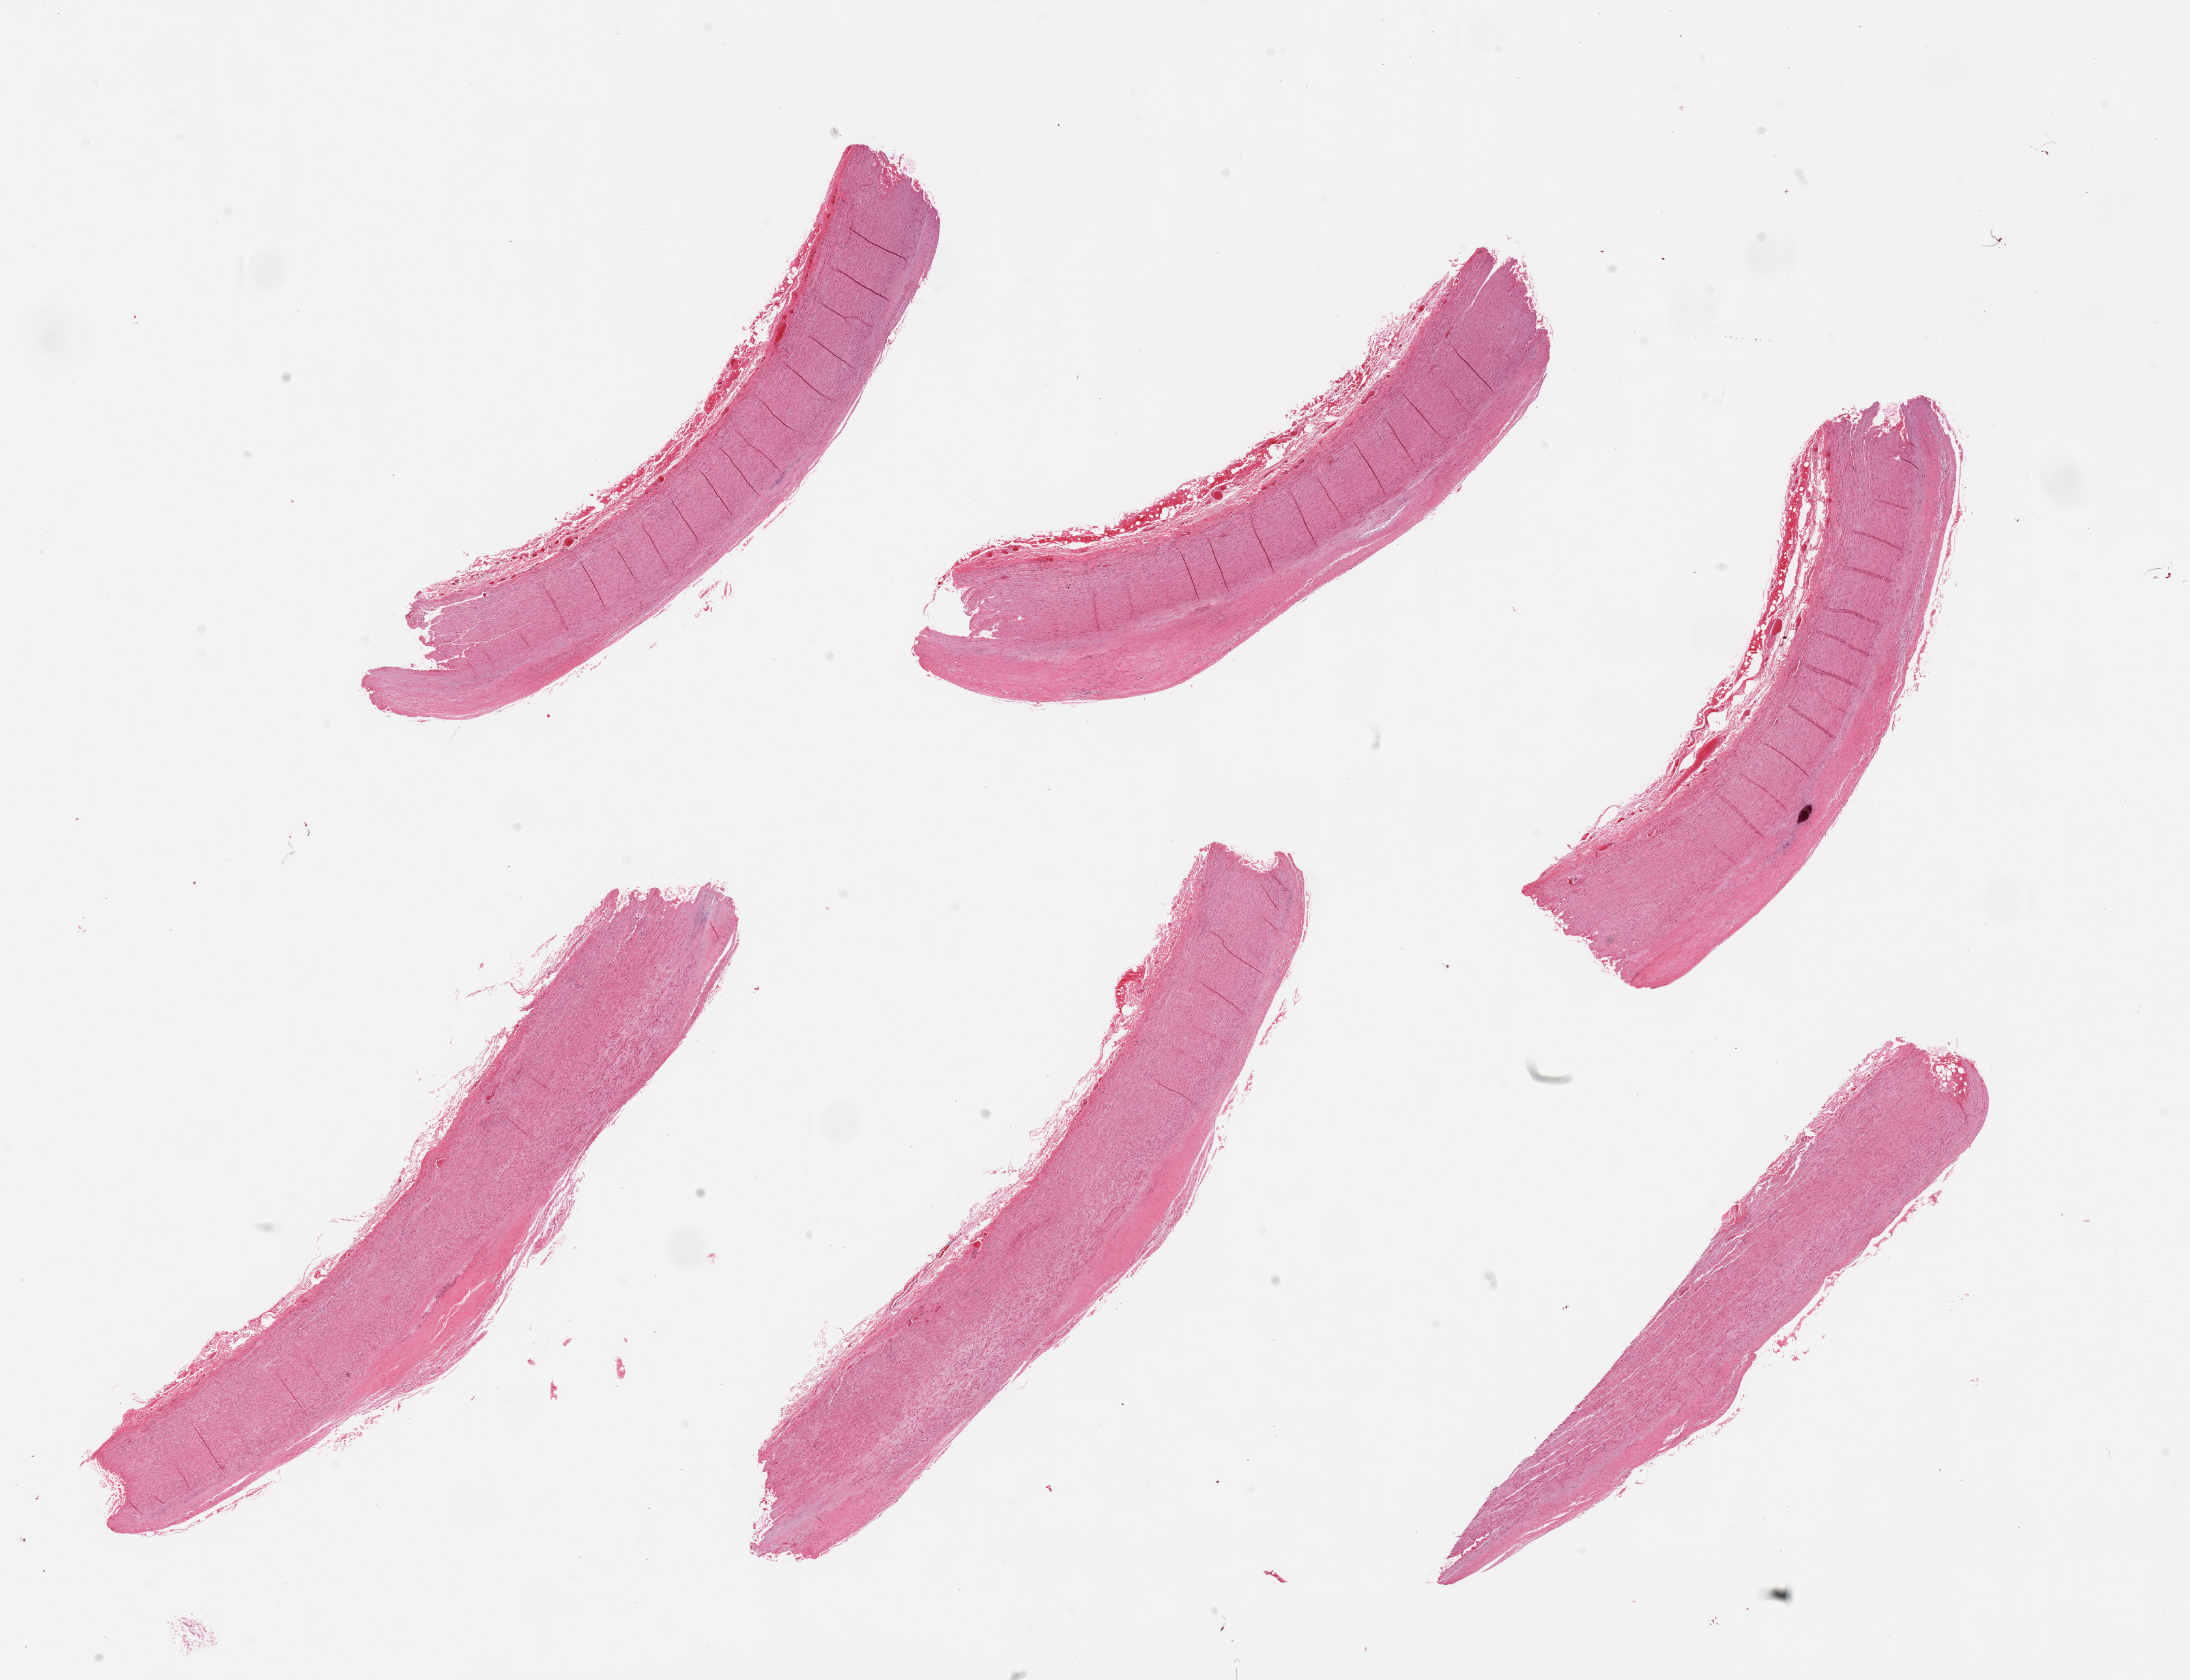
Whole-slide image, H&E stain, brightfield — whole scanned area (about 26.6 x 20.4 mm) shown as a low-resolution overview, PAXgene-fixed paraffin-embedded (PFPE) section, target tissue: aorta, tissue donor sample. Donor: male.
- reviewer comment on this tissue sample: 6 pieces, minimal adherent fat, marked atherotic deposition, up to ~0.75mm